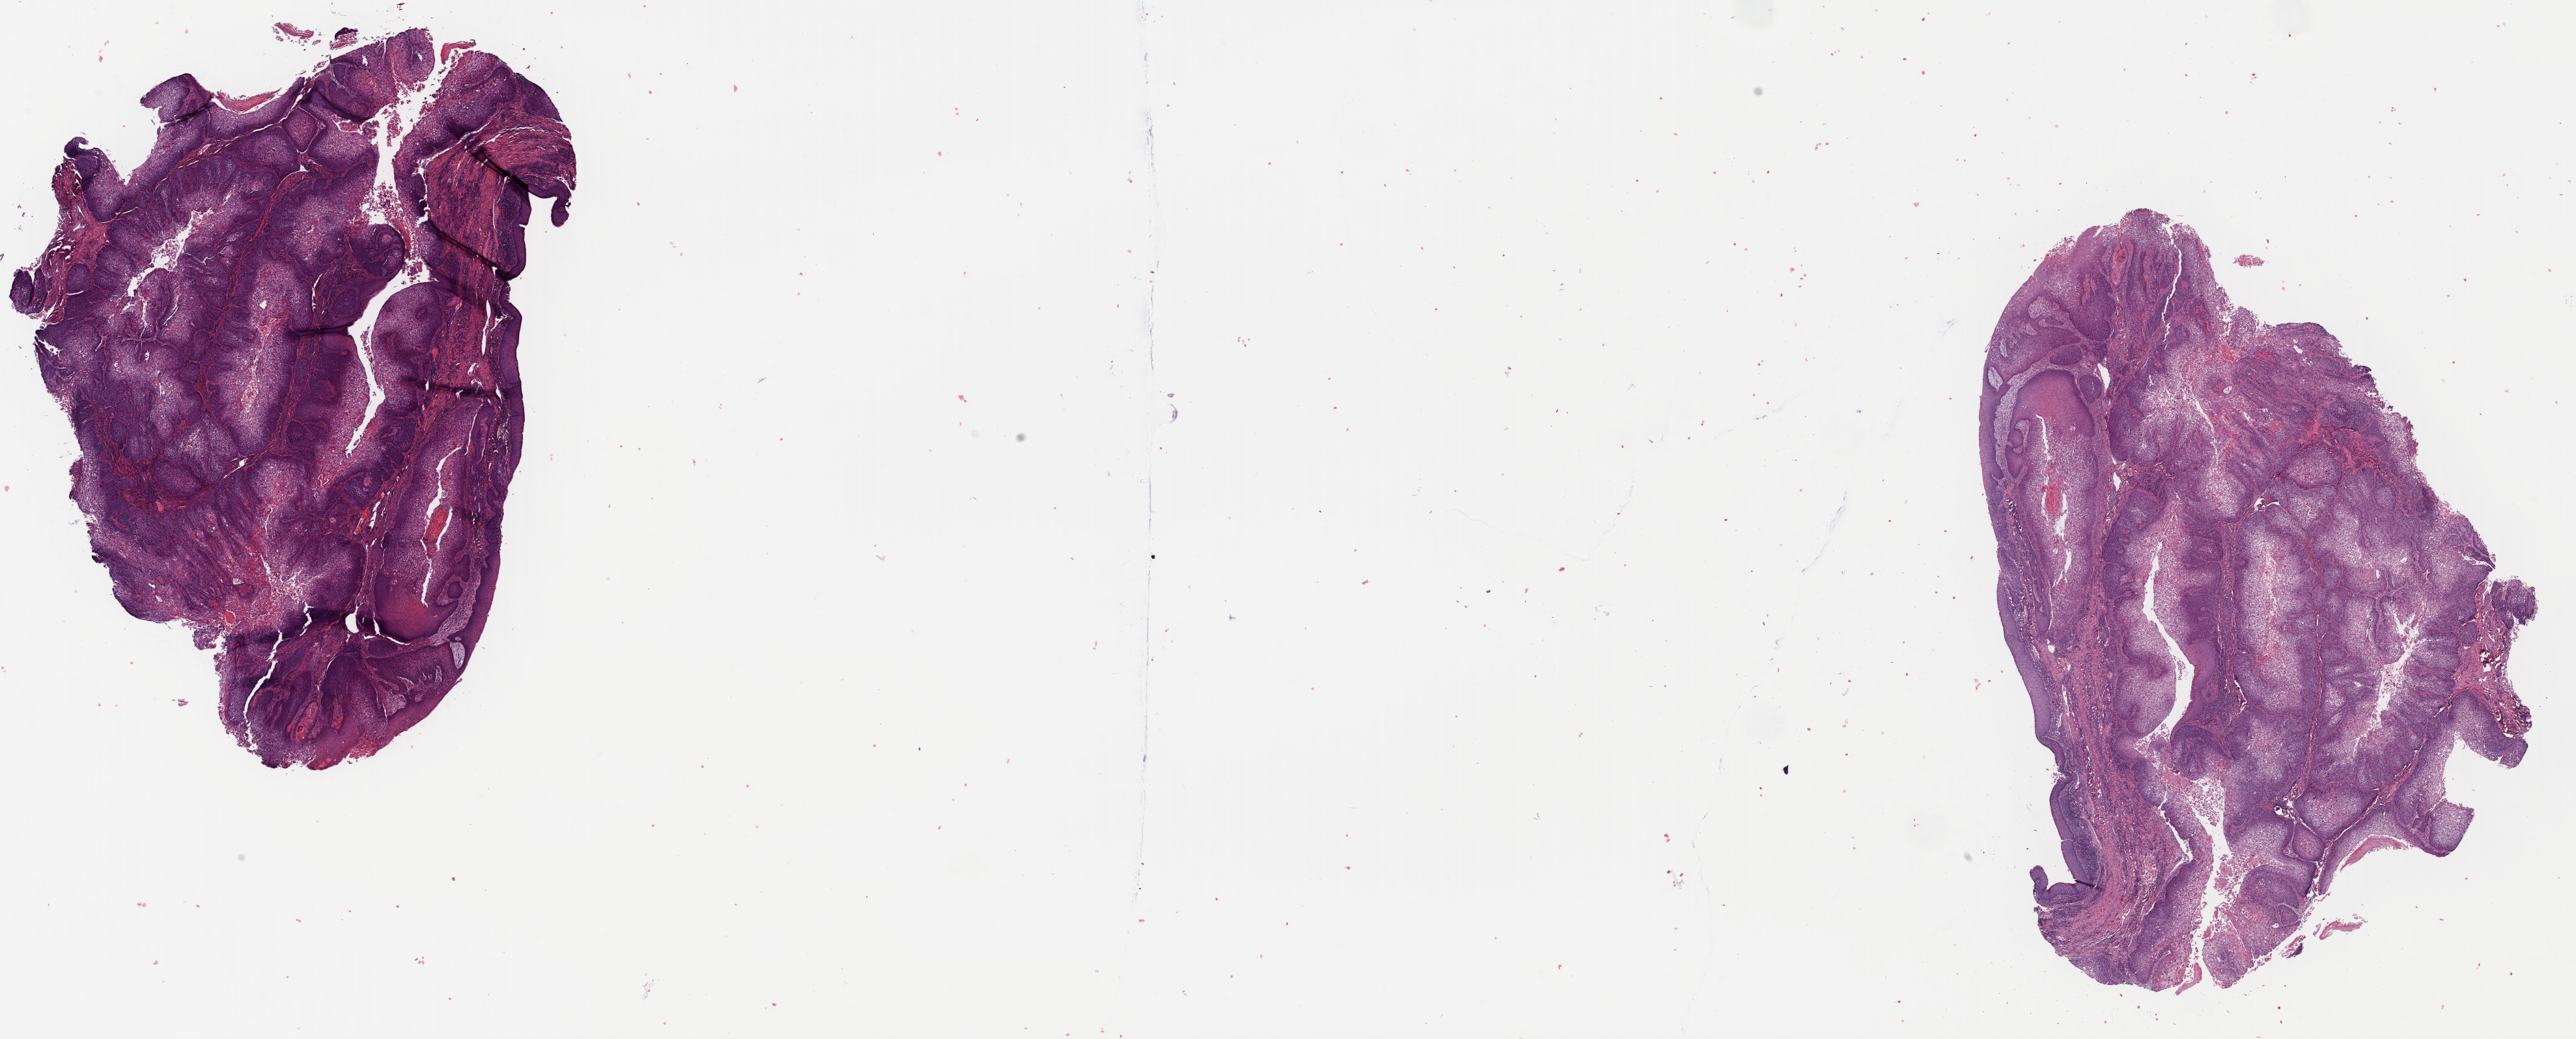
Hematoxylin and eosin (H&E) stained whole-slide image — a low-resolution overview of the entire scanned area, about 31.1 x 12.5 mm (slide scanned at 40x). FFPE section. Head and neck, primary tumour sample. Patient: male, age at initial diagnosis 65 years. Histologic grade: G2 (moderately differentiated).
• AJCC pathologic stage: II
• pathologic diagnosis: Squamous cell carcinoma, keratinizing, NOS (larynx, NOS)
• laterality: right
• TNM: T2 N0 M0